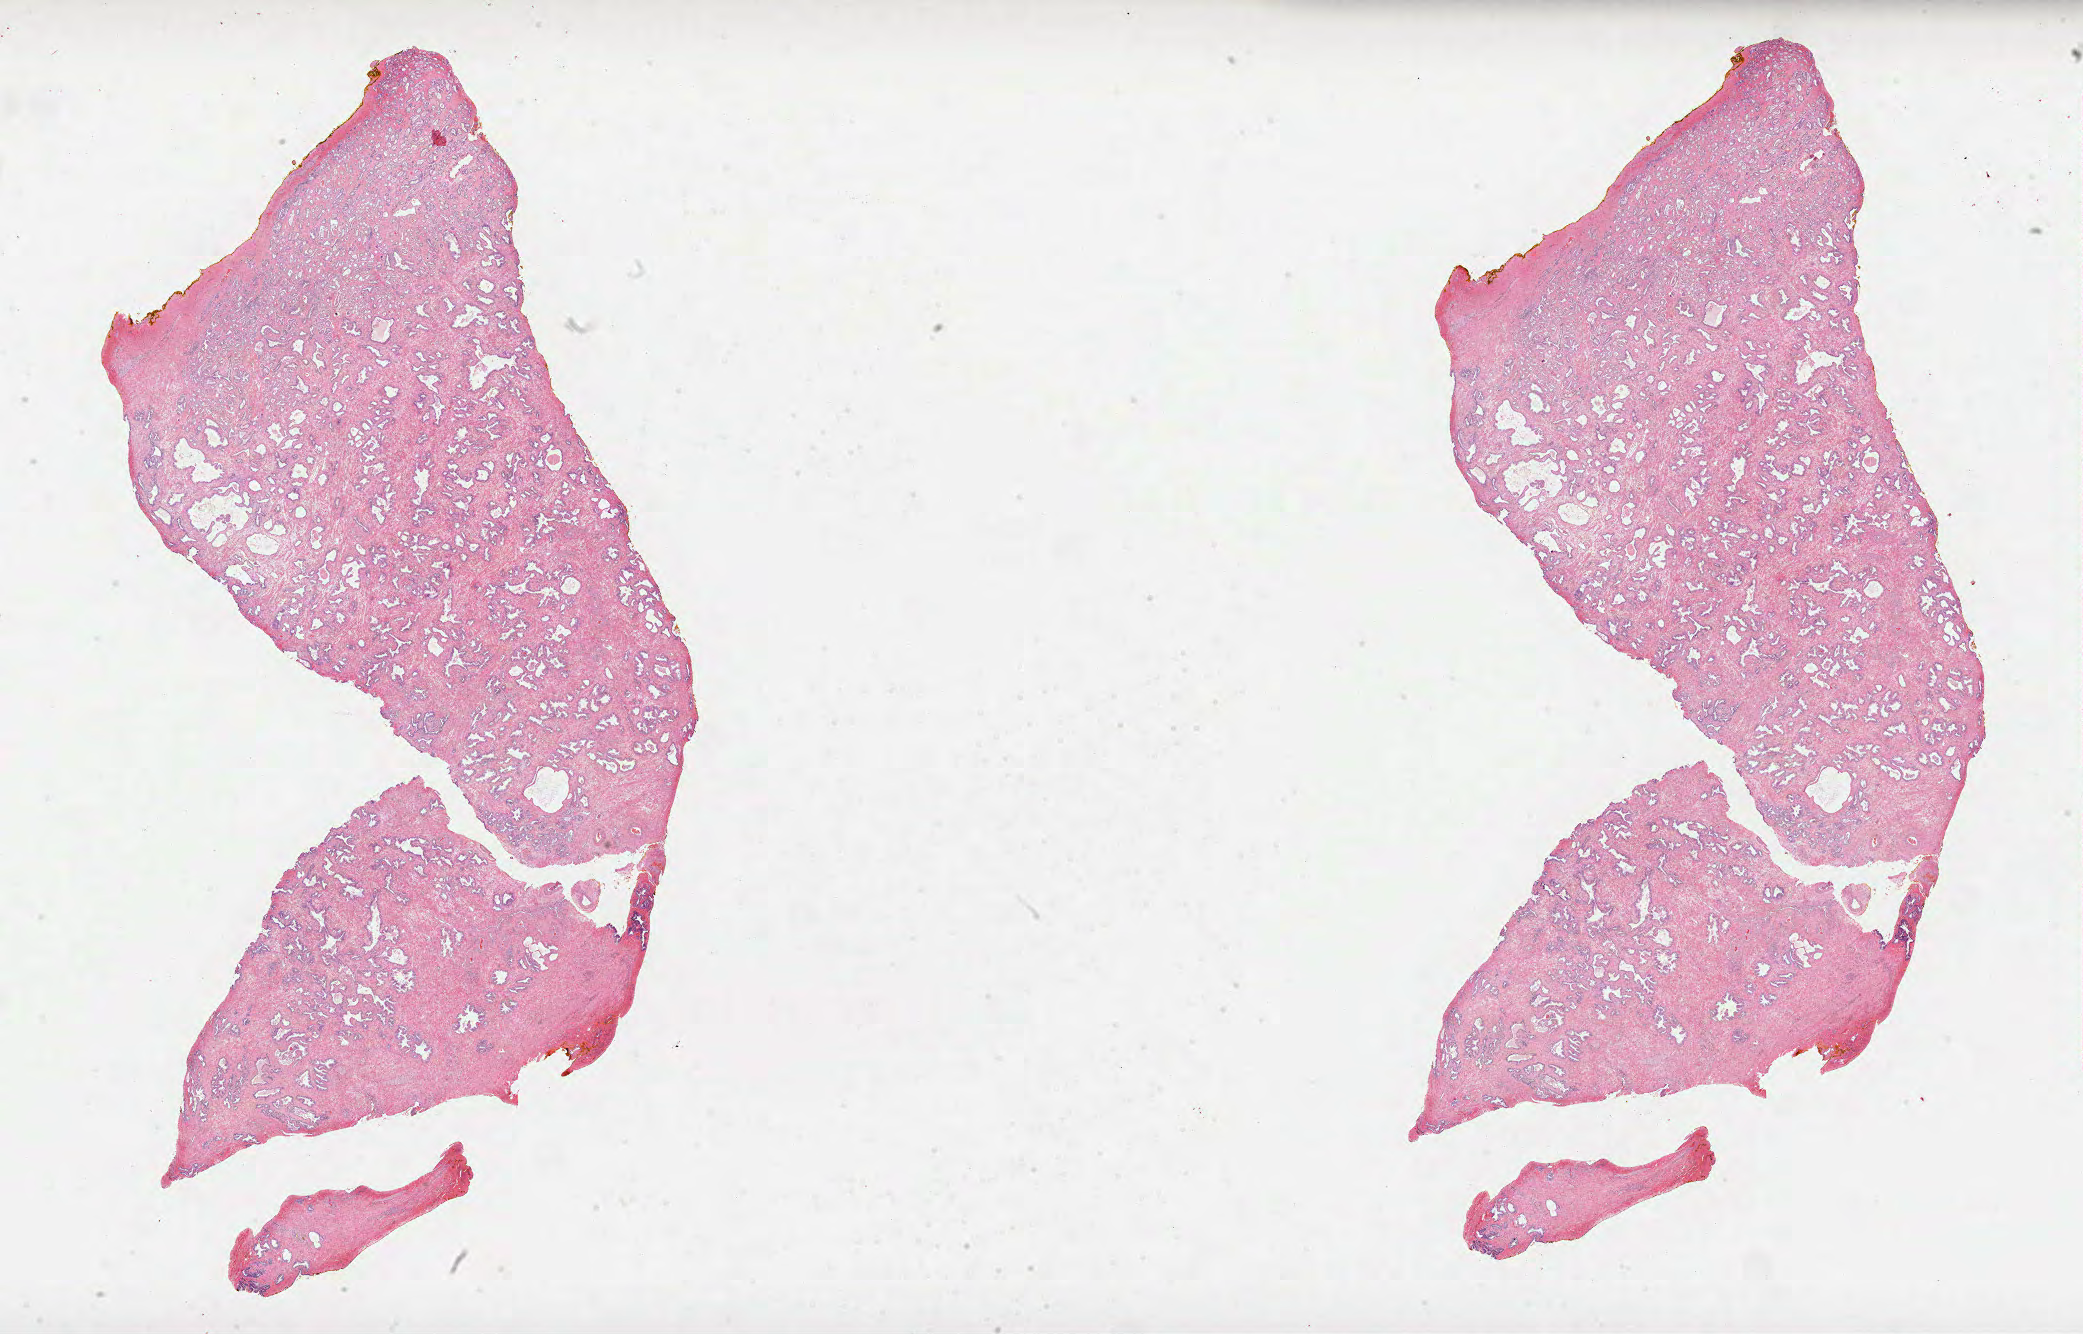
Digitized H&E tissue section (whole slide), a low-resolution overview of the entire scanned area, about 33.6 x 21.5 mm (slide scanned at 40x); formalin-fixed paraffin-embedded (FFPE) diagnostic section; sample: primary tumour, prostate. Male, age 51 years at initial diagnosis. Gleason score: 7 (3+4).
Histologic diagnosis: Acinar cell carcinoma (prostate gland).